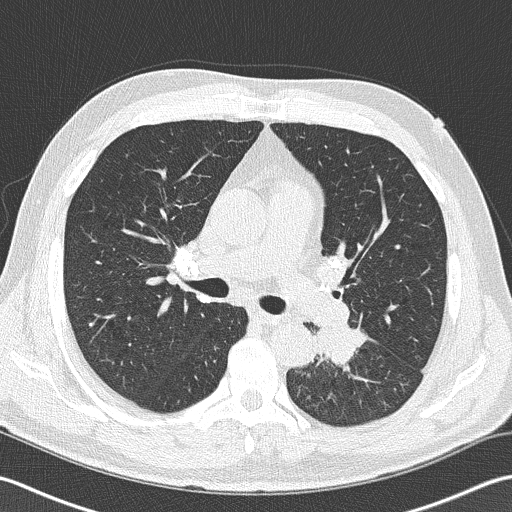
Chest CT (low-dose screening protocol), one axial image, second screening round (one year after baseline), lung window (W 1500 / L -600 HU), 2 mm slice thickness, slice 65 of 170 in the series. Male, age 57 years at enrolment.
Expert-annotated lung lesion, bounding box (x1, y1, x2, y2) in pixels: (294, 309, 374, 384). The exam's reader record, not a measurement of the box and not confirmed to be the same lesion: non-calcified nodule or mass ≥4 mm, left lower lobe, 40 × 30 mm, spiculated (stellate) margins, soft tissue attenuation, pre-existing on the prior screen: no. Official screen result: positive, other. Participant outcome: lung cancer diagnosed 9 days after this screen — squamous cell carcinoma, NOS, left lower lobe, moderately differentiated (G2), stage IIIB (AJCC 6th edition), 38 mm at pathology.